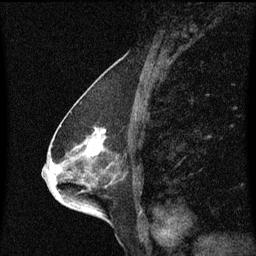
Breast MRI (dynamic contrast-enhanced), one sagittal slice. Slice 32 of 60 in the series (ordered by position). Dynamic contrast-enhanced series, image 2 of 3 at this slice position (ordered by acquisition). 1.5 T. TE 4.2 ms, TR 8.4 ms. 256 × 256 image matrix, field of view 200 × 200 mm. Female patient, age 68 years. Case-level facts recorded for this patient, not image findings: setting: breast cancer imaged before/during neoadjuvant chemotherapy; receptor status: triple-negative.
Structures marked on this image (semi-automatically segmented with operator editing):
- analysis volume of interest (the breast-tissue region the enhancement analysis was run in; not a lesion): bounding box <41,114,132,203> (left, top, right, bottom; pixels)
- tumour enhancement mask (voxels above the 70 % enhancement threshold inside the analysis volume of interest): <52,142,103,173>